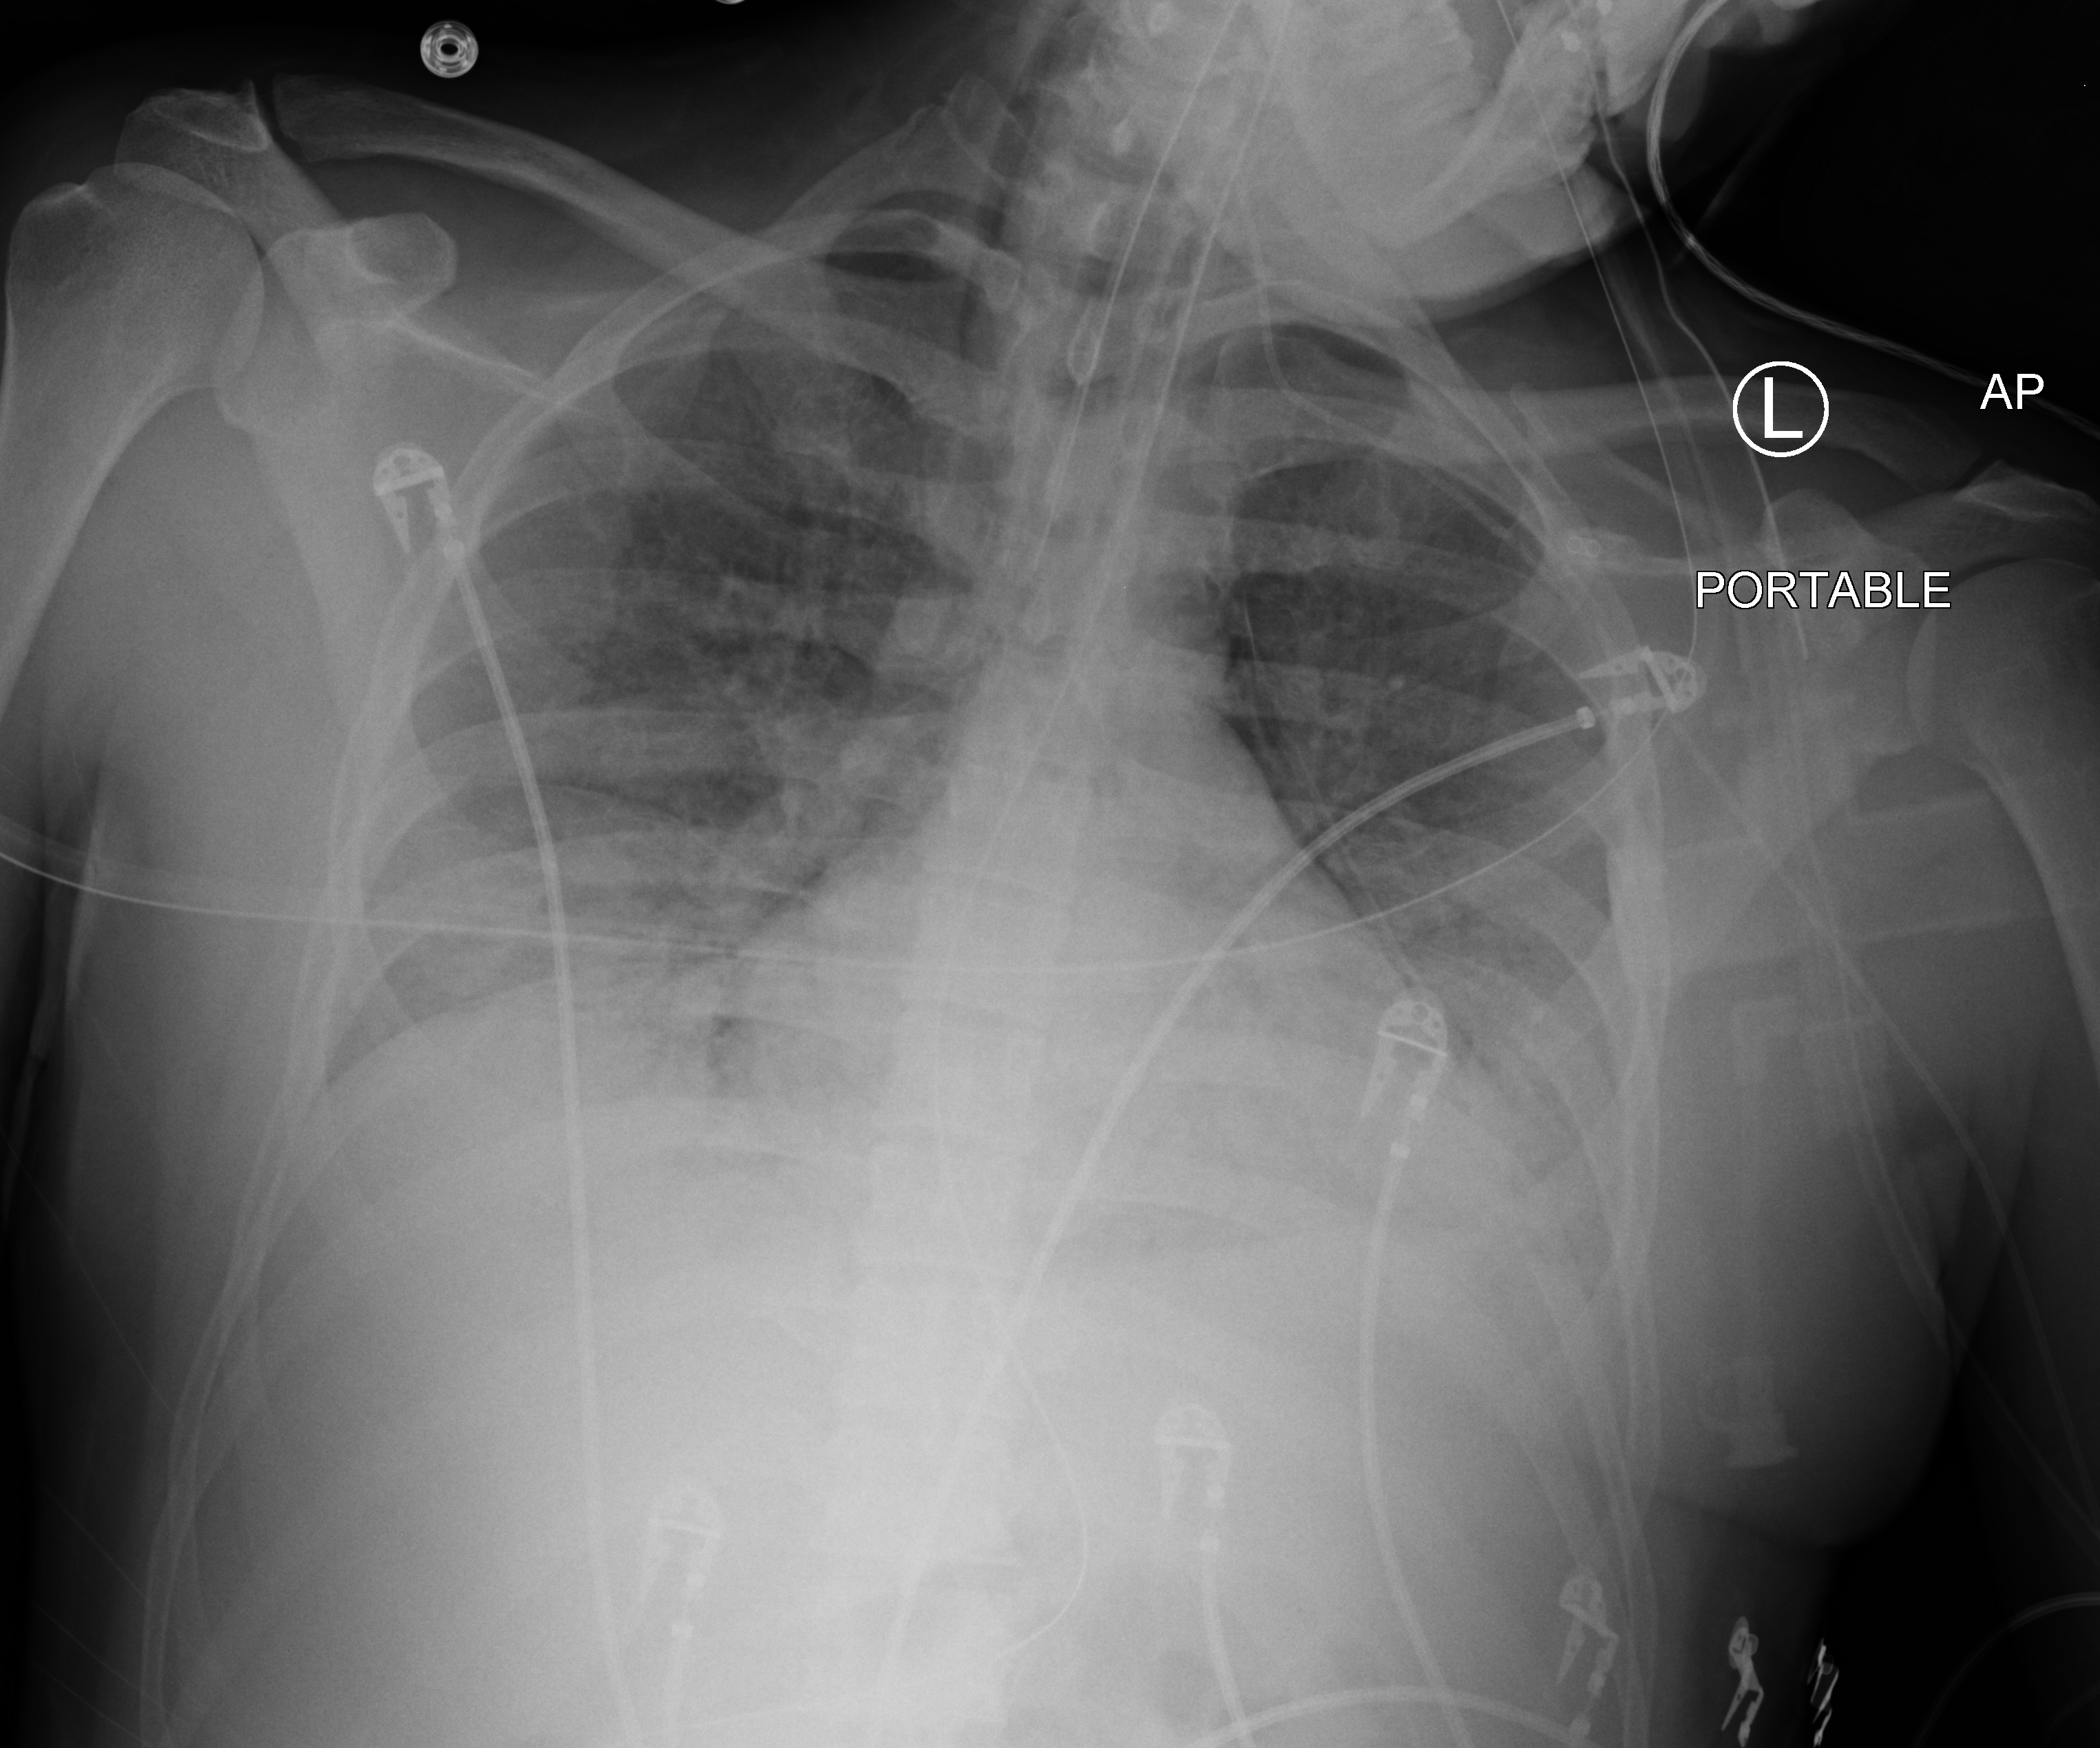
Bedside chest radiograph (computed radiography); anteroposterior (AP) projection. Male patient hospitalised with COVID-19, age 18–59 years.
Hospital-stay facts (about this admission, not read from this image; timing relative to this image not recorded):
- admitted to intensive care during this hospital stay: yes
- mechanically ventilated during this hospital stay: yes